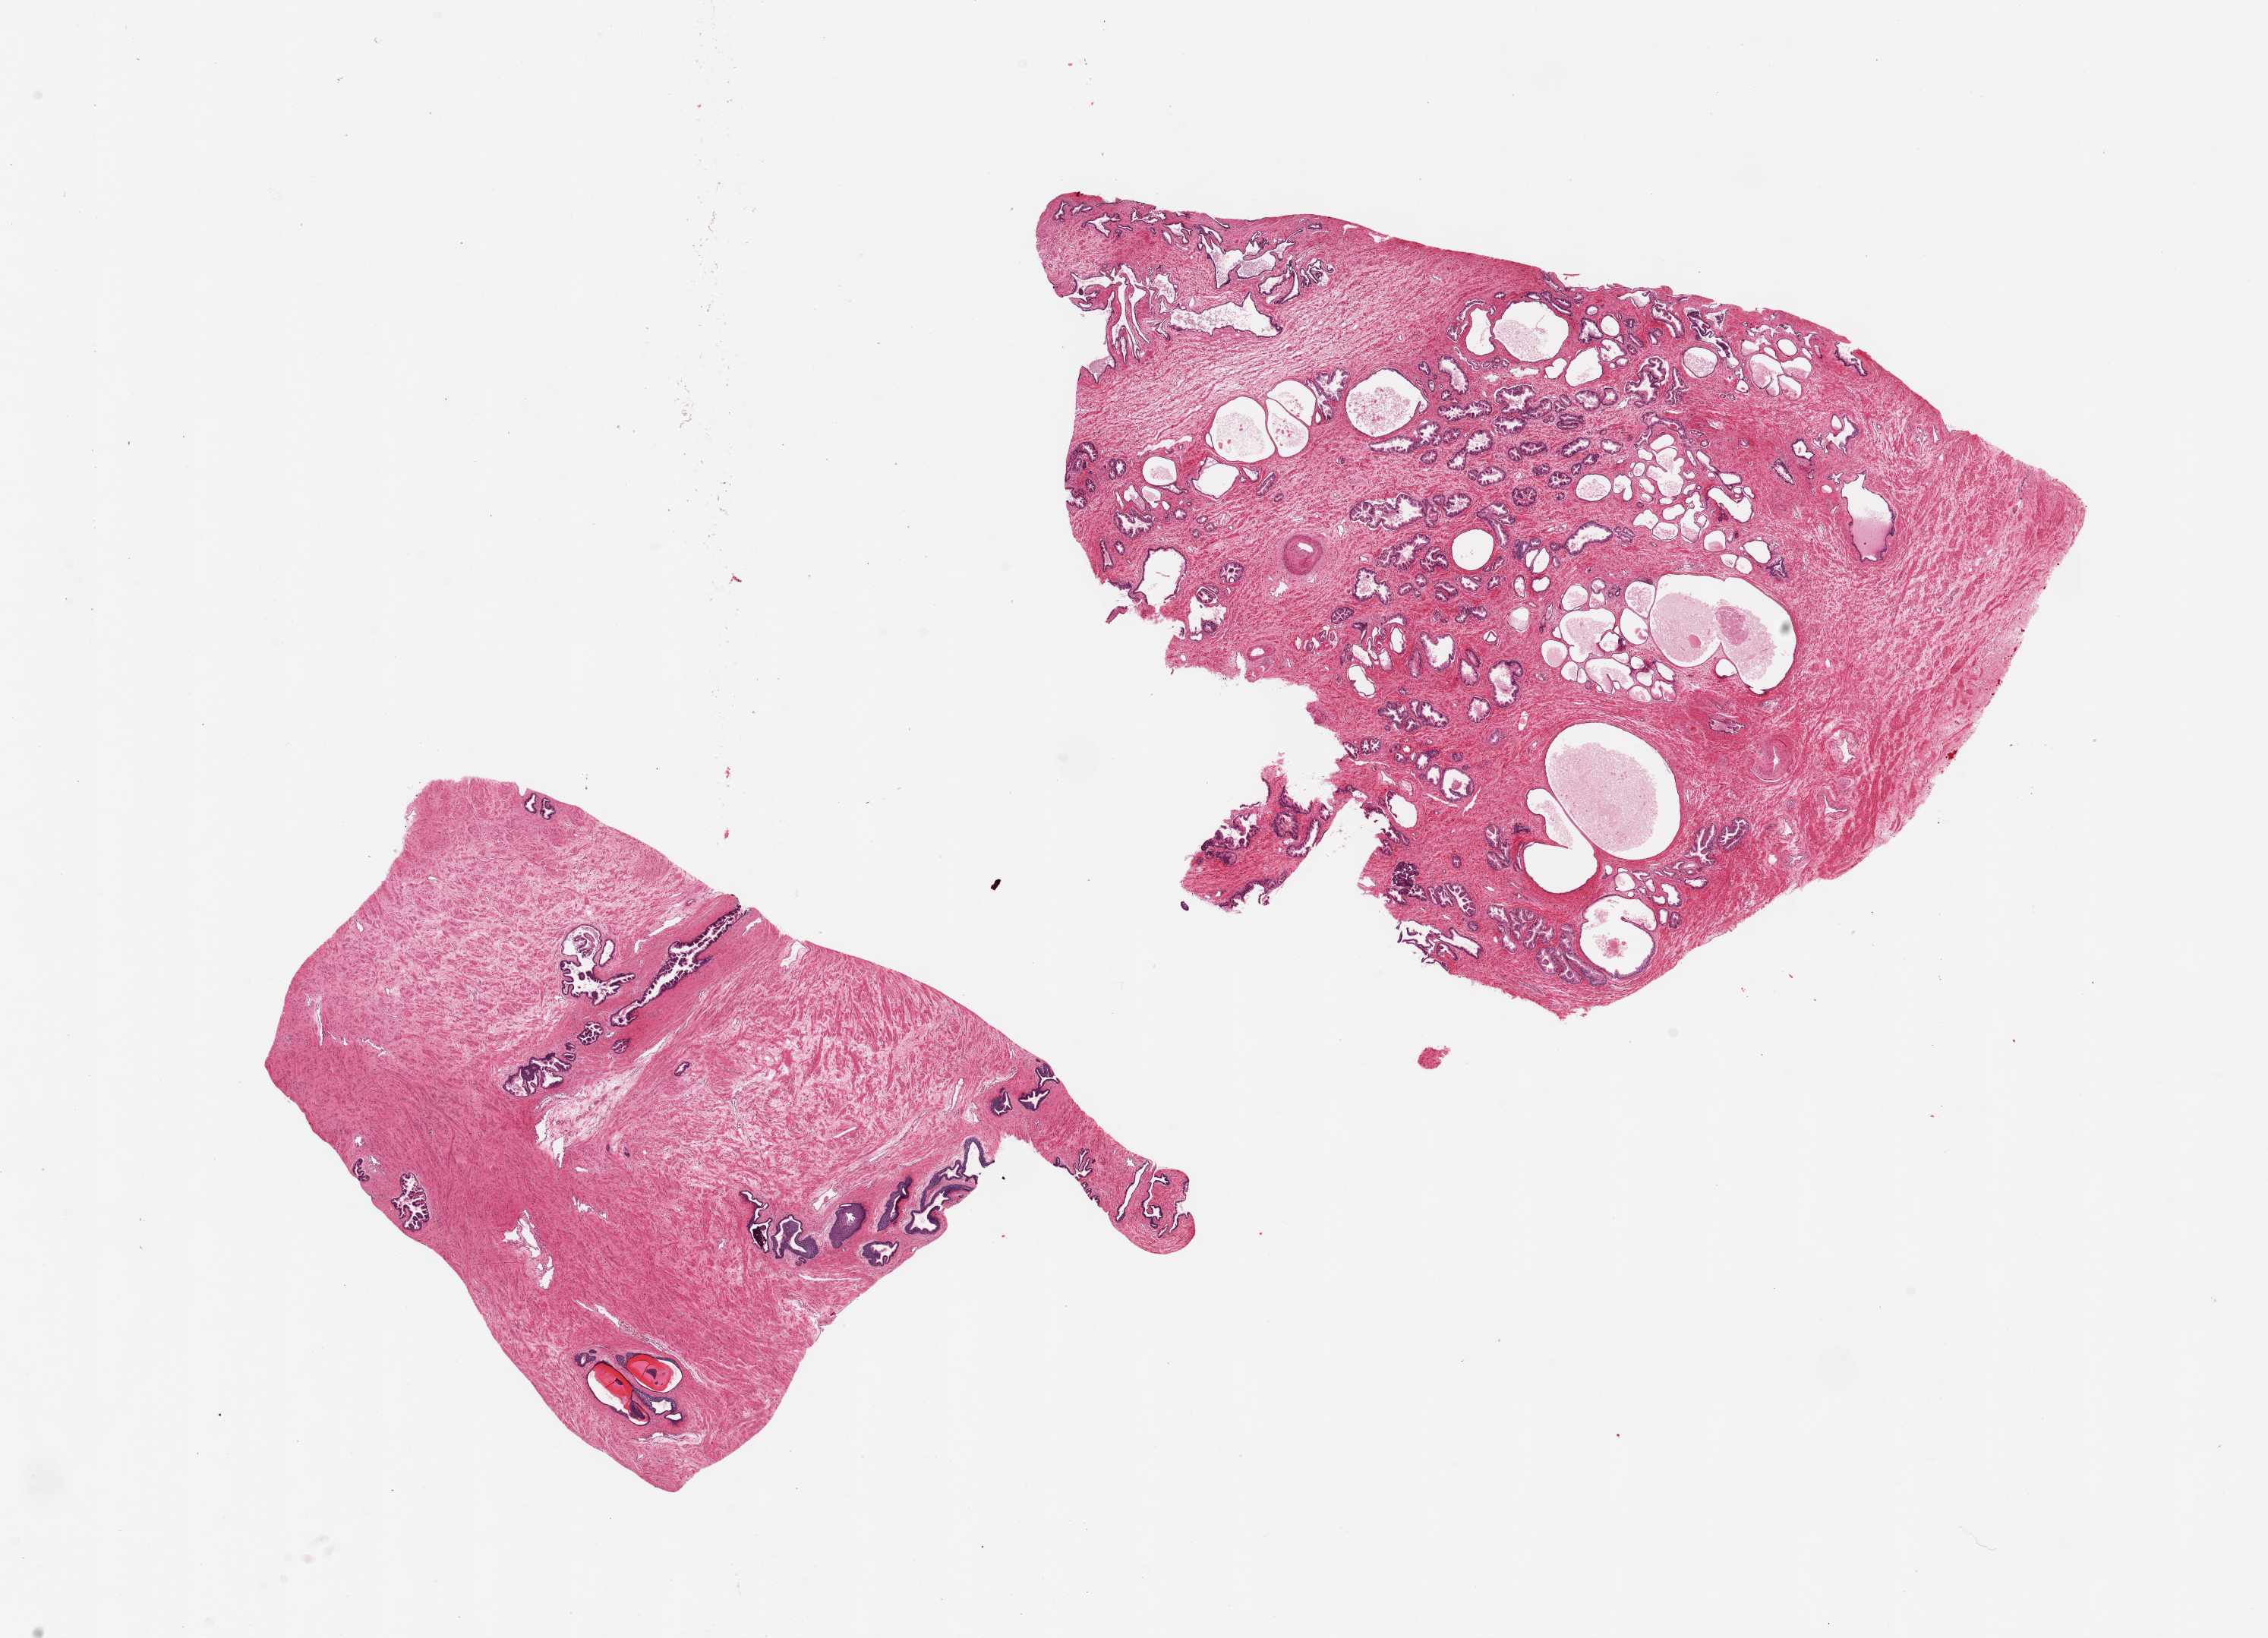
Whole-slide image, haematoxylin and eosin stain, brightfield, a low-resolution overview of the entire scanned area, about 23.6 x 17.1 mm (slide scanned at 20x); PAXgene-fixed paraffin-embedded (PFPE) section; sampled site (target tissue): prostate; tissue donor sample. Male donor.
Reviewer comment on this tissue sample: 2 pieces, ~9x7mm glandular hyperplasia and cystic atrophy.